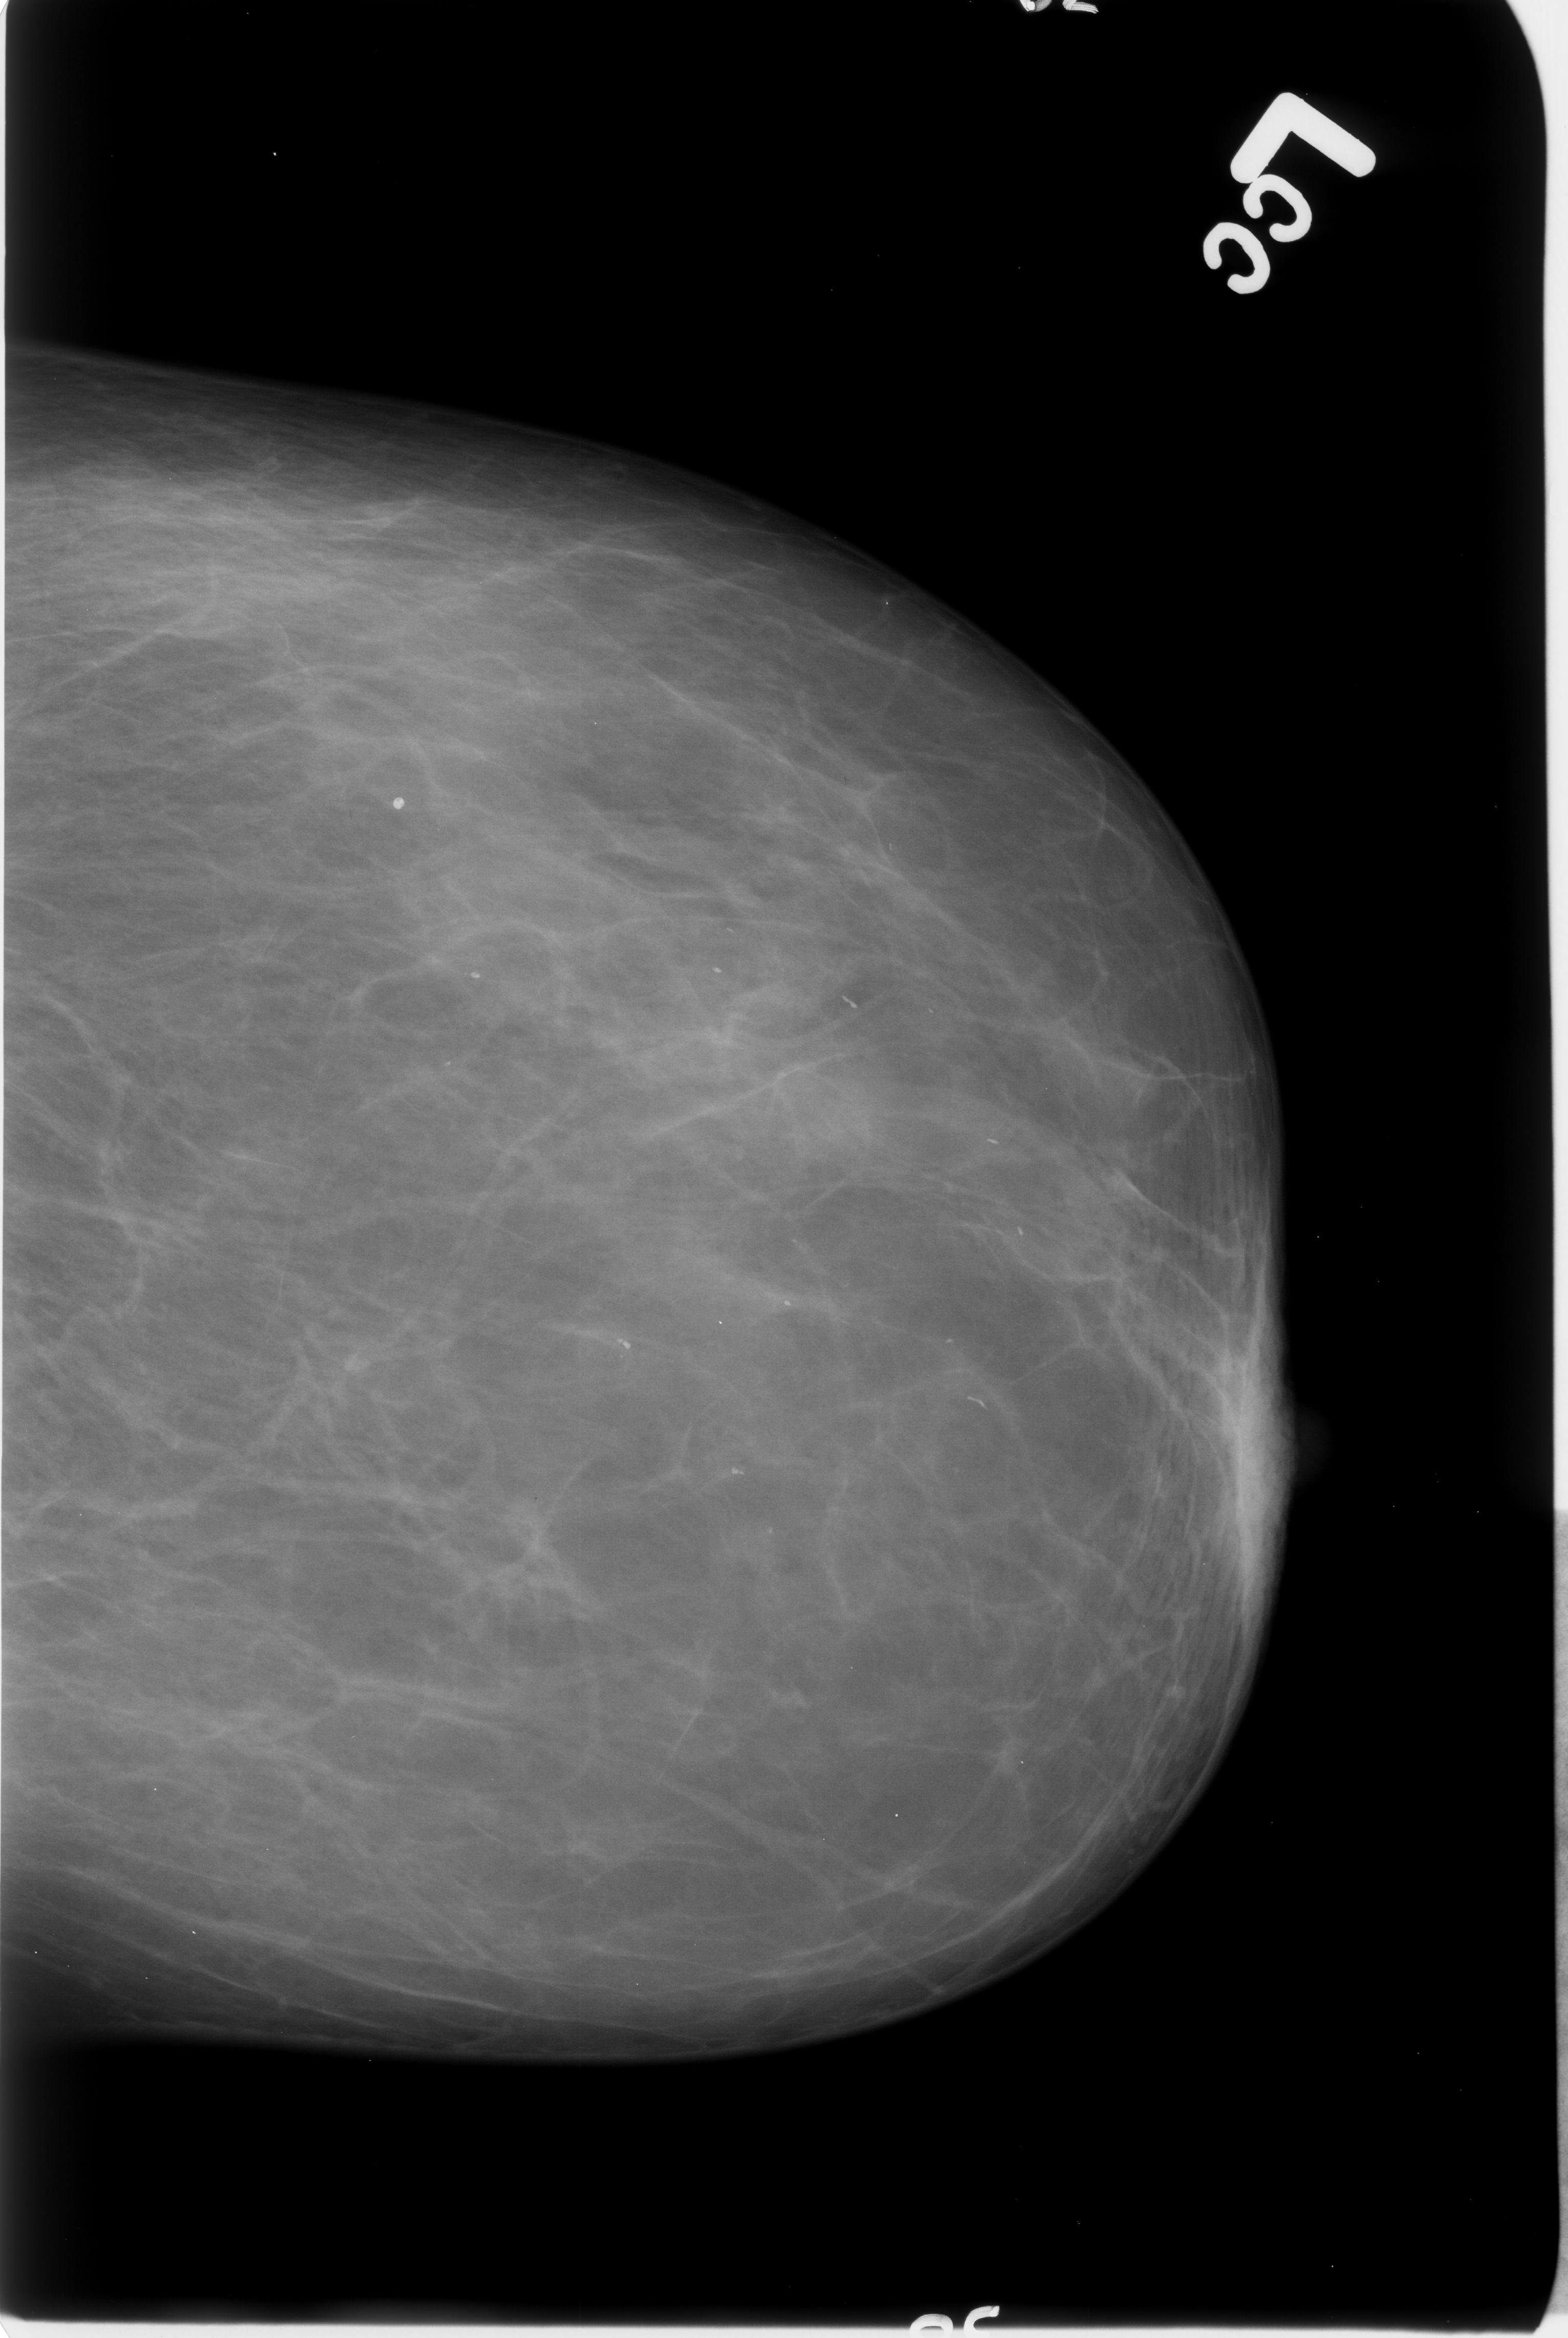
Scanned film-screen mammogram; left breast; CC view; breast composition: almost entirely fatty (BI-RADS density category 1 of 4); 1568 × 2338 image matrix.
Expert-marked regions of interest on this image (one box per marked abnormality):
- Finding 1 of 3: calcifications, distribution regional; BI-RADS assessment category 2; outcome (as recorded, no biopsy): benign without callback (not worked up further): bounding box <802,974,873,1037> (left, top, right, bottom; pixels)
- Finding 2 of 3: calcifications, distribution regional; BI-RADS assessment category 2; subtlety rating 3 on a 1 (subtle) to 5 (obvious) scale; outcome (as recorded, no biopsy): benign without callback (not worked up further): <949,1375,1020,1442>
- Finding 3 of 3: calcifications, distribution regional; BI-RADS assessment category 2; benign; no additional work-up was recommended (outcome (as recorded, no biopsy): benign without callback): <966,1130,1020,1168>